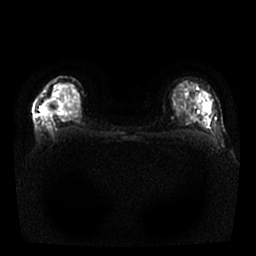
Breast MRI, one axial slice; position 14 of 25 along the scan axis; diffusion-weighted series; image 2 of 4 stored at this slice position (different b-values; order by instance number); 1.5 T; 4 mm slice thickness; 256 × 256 image matrix. Female patient.
Annotated regions visible in this slice (manually delineated by an expert):
- tumour on diffusion-weighted imaging: bounding box [x1, y1, x2, y2] px = [42, 110, 45, 114]